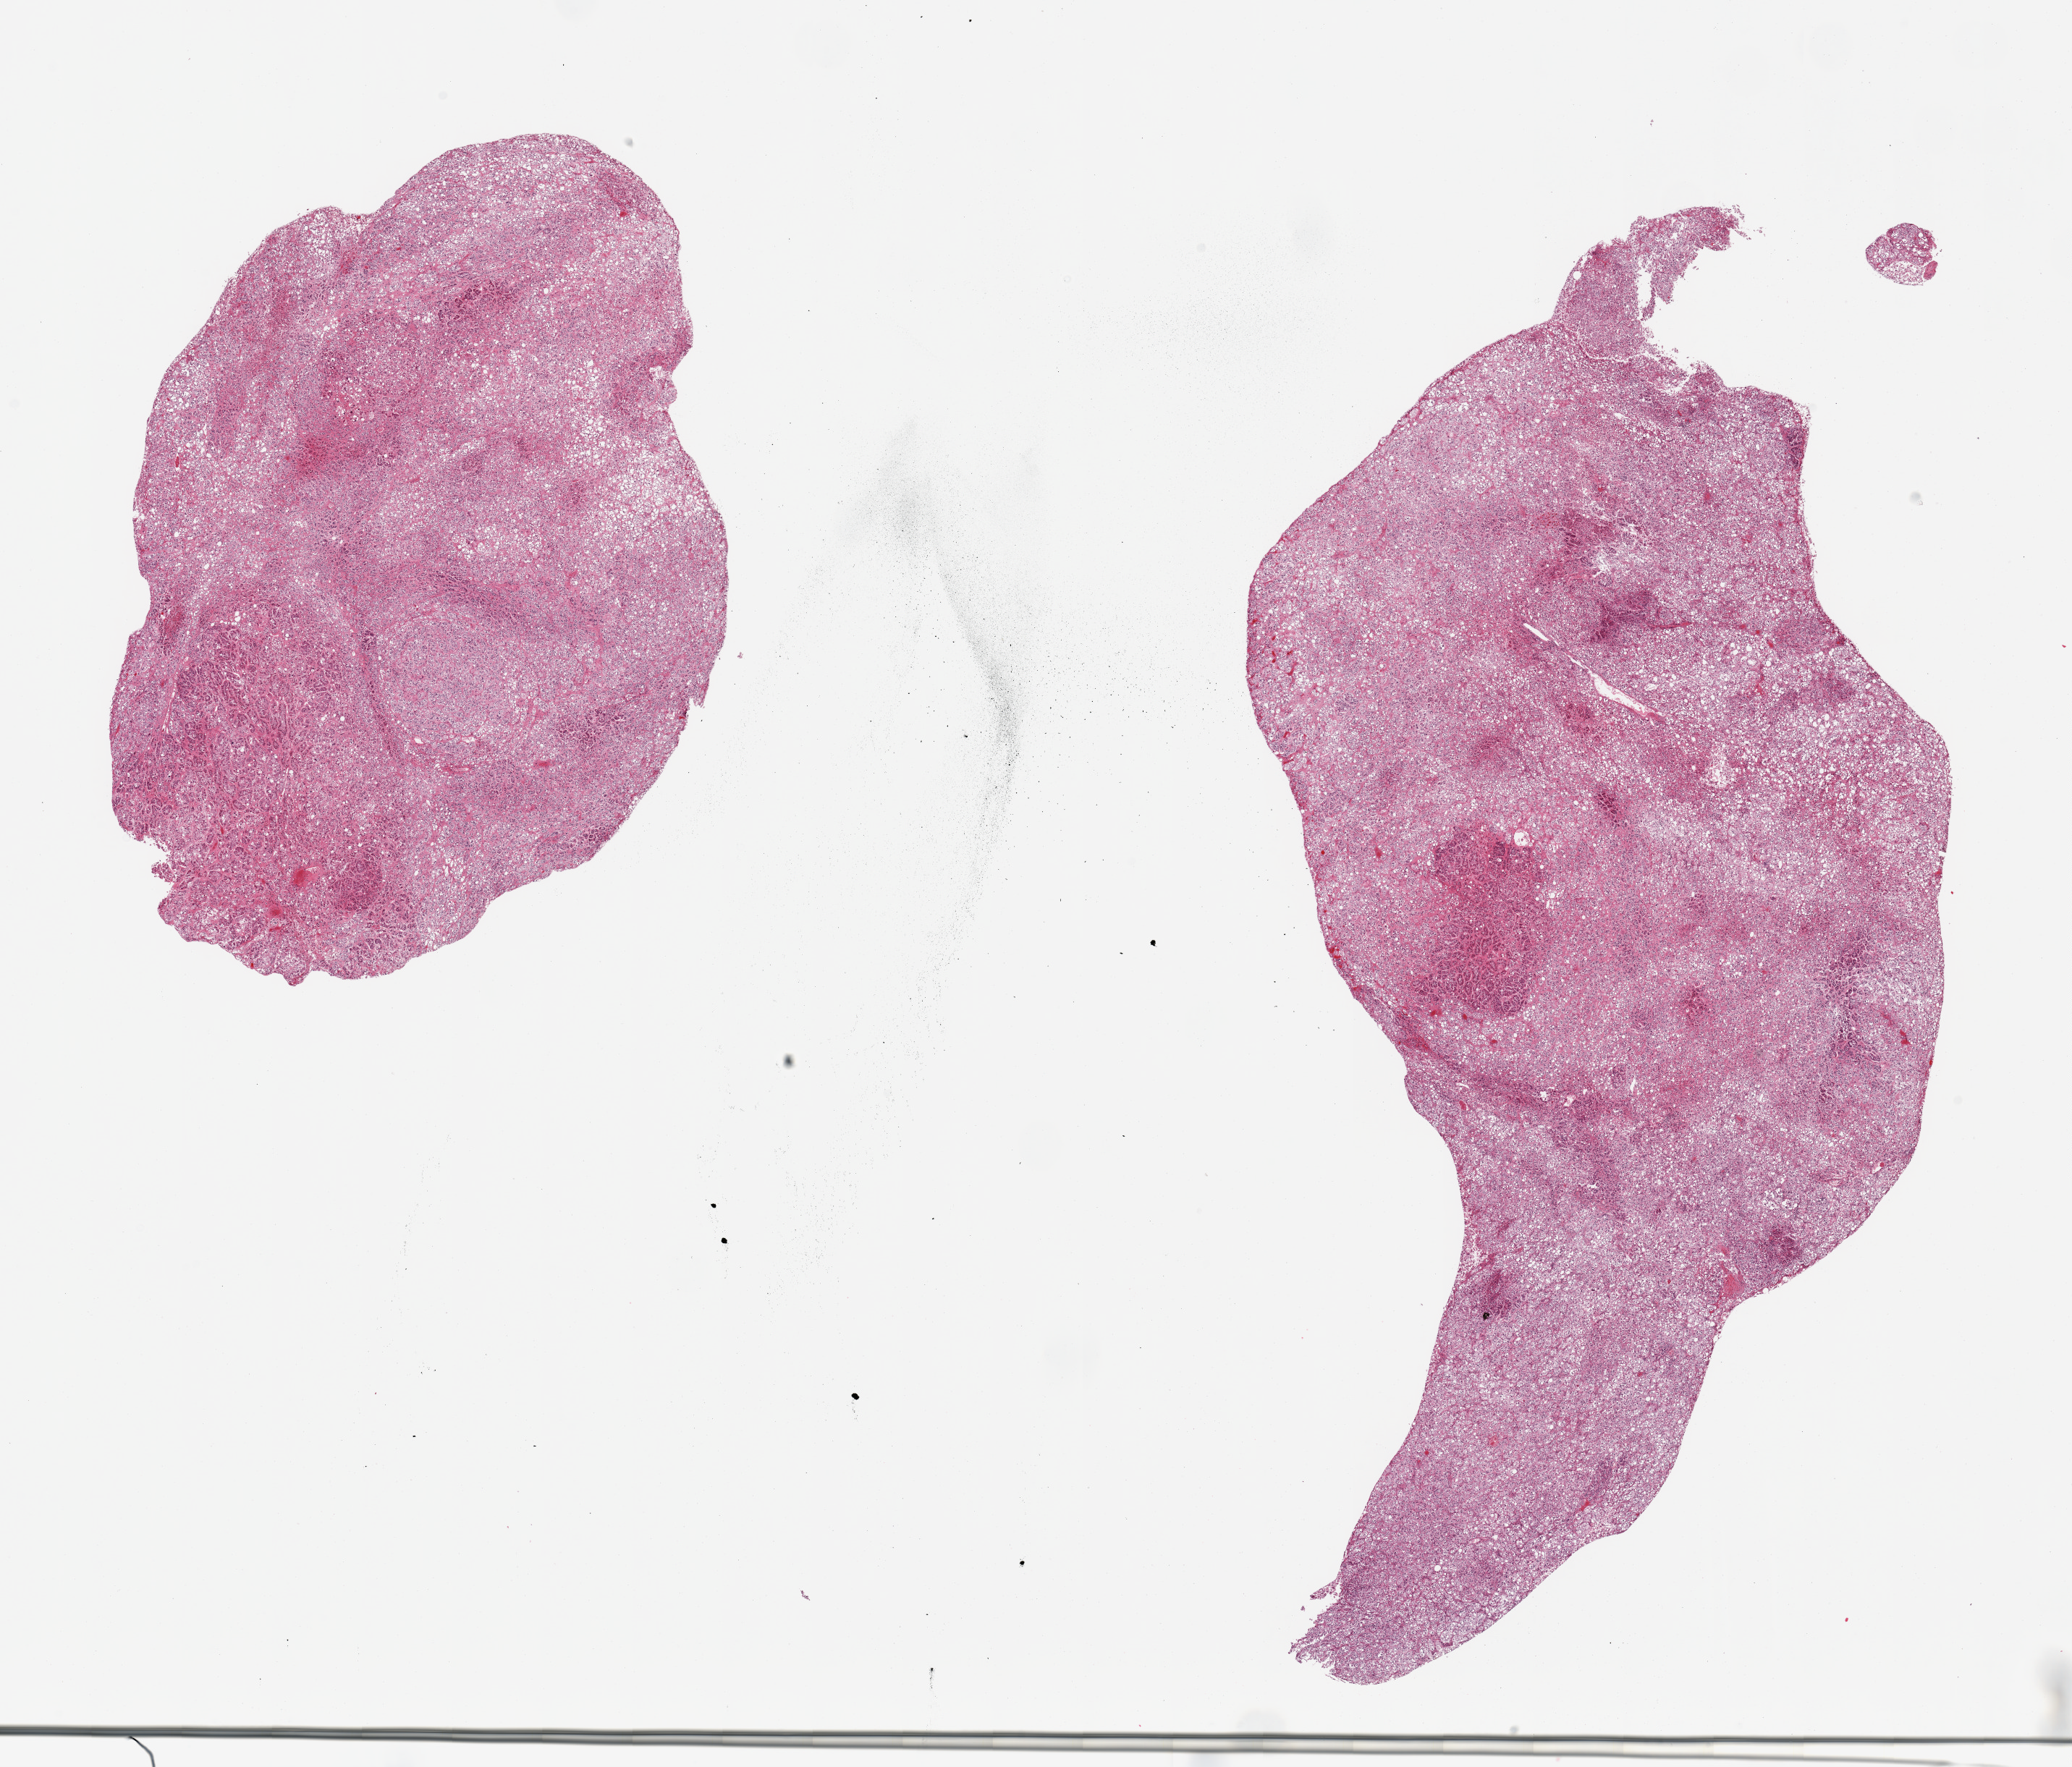
Whole-slide image, hematoxylin and eosin (H&E) stain — low-resolution overview of the scanned area, about 22.6 x 19.3 mm; PAXgene-fixed paraffin-embedded (PFPE) section; section of adrenal gland (target tissue); donor tissue sample.
Reviewer comment on this tissue sample: 2 pieces, all cortex.